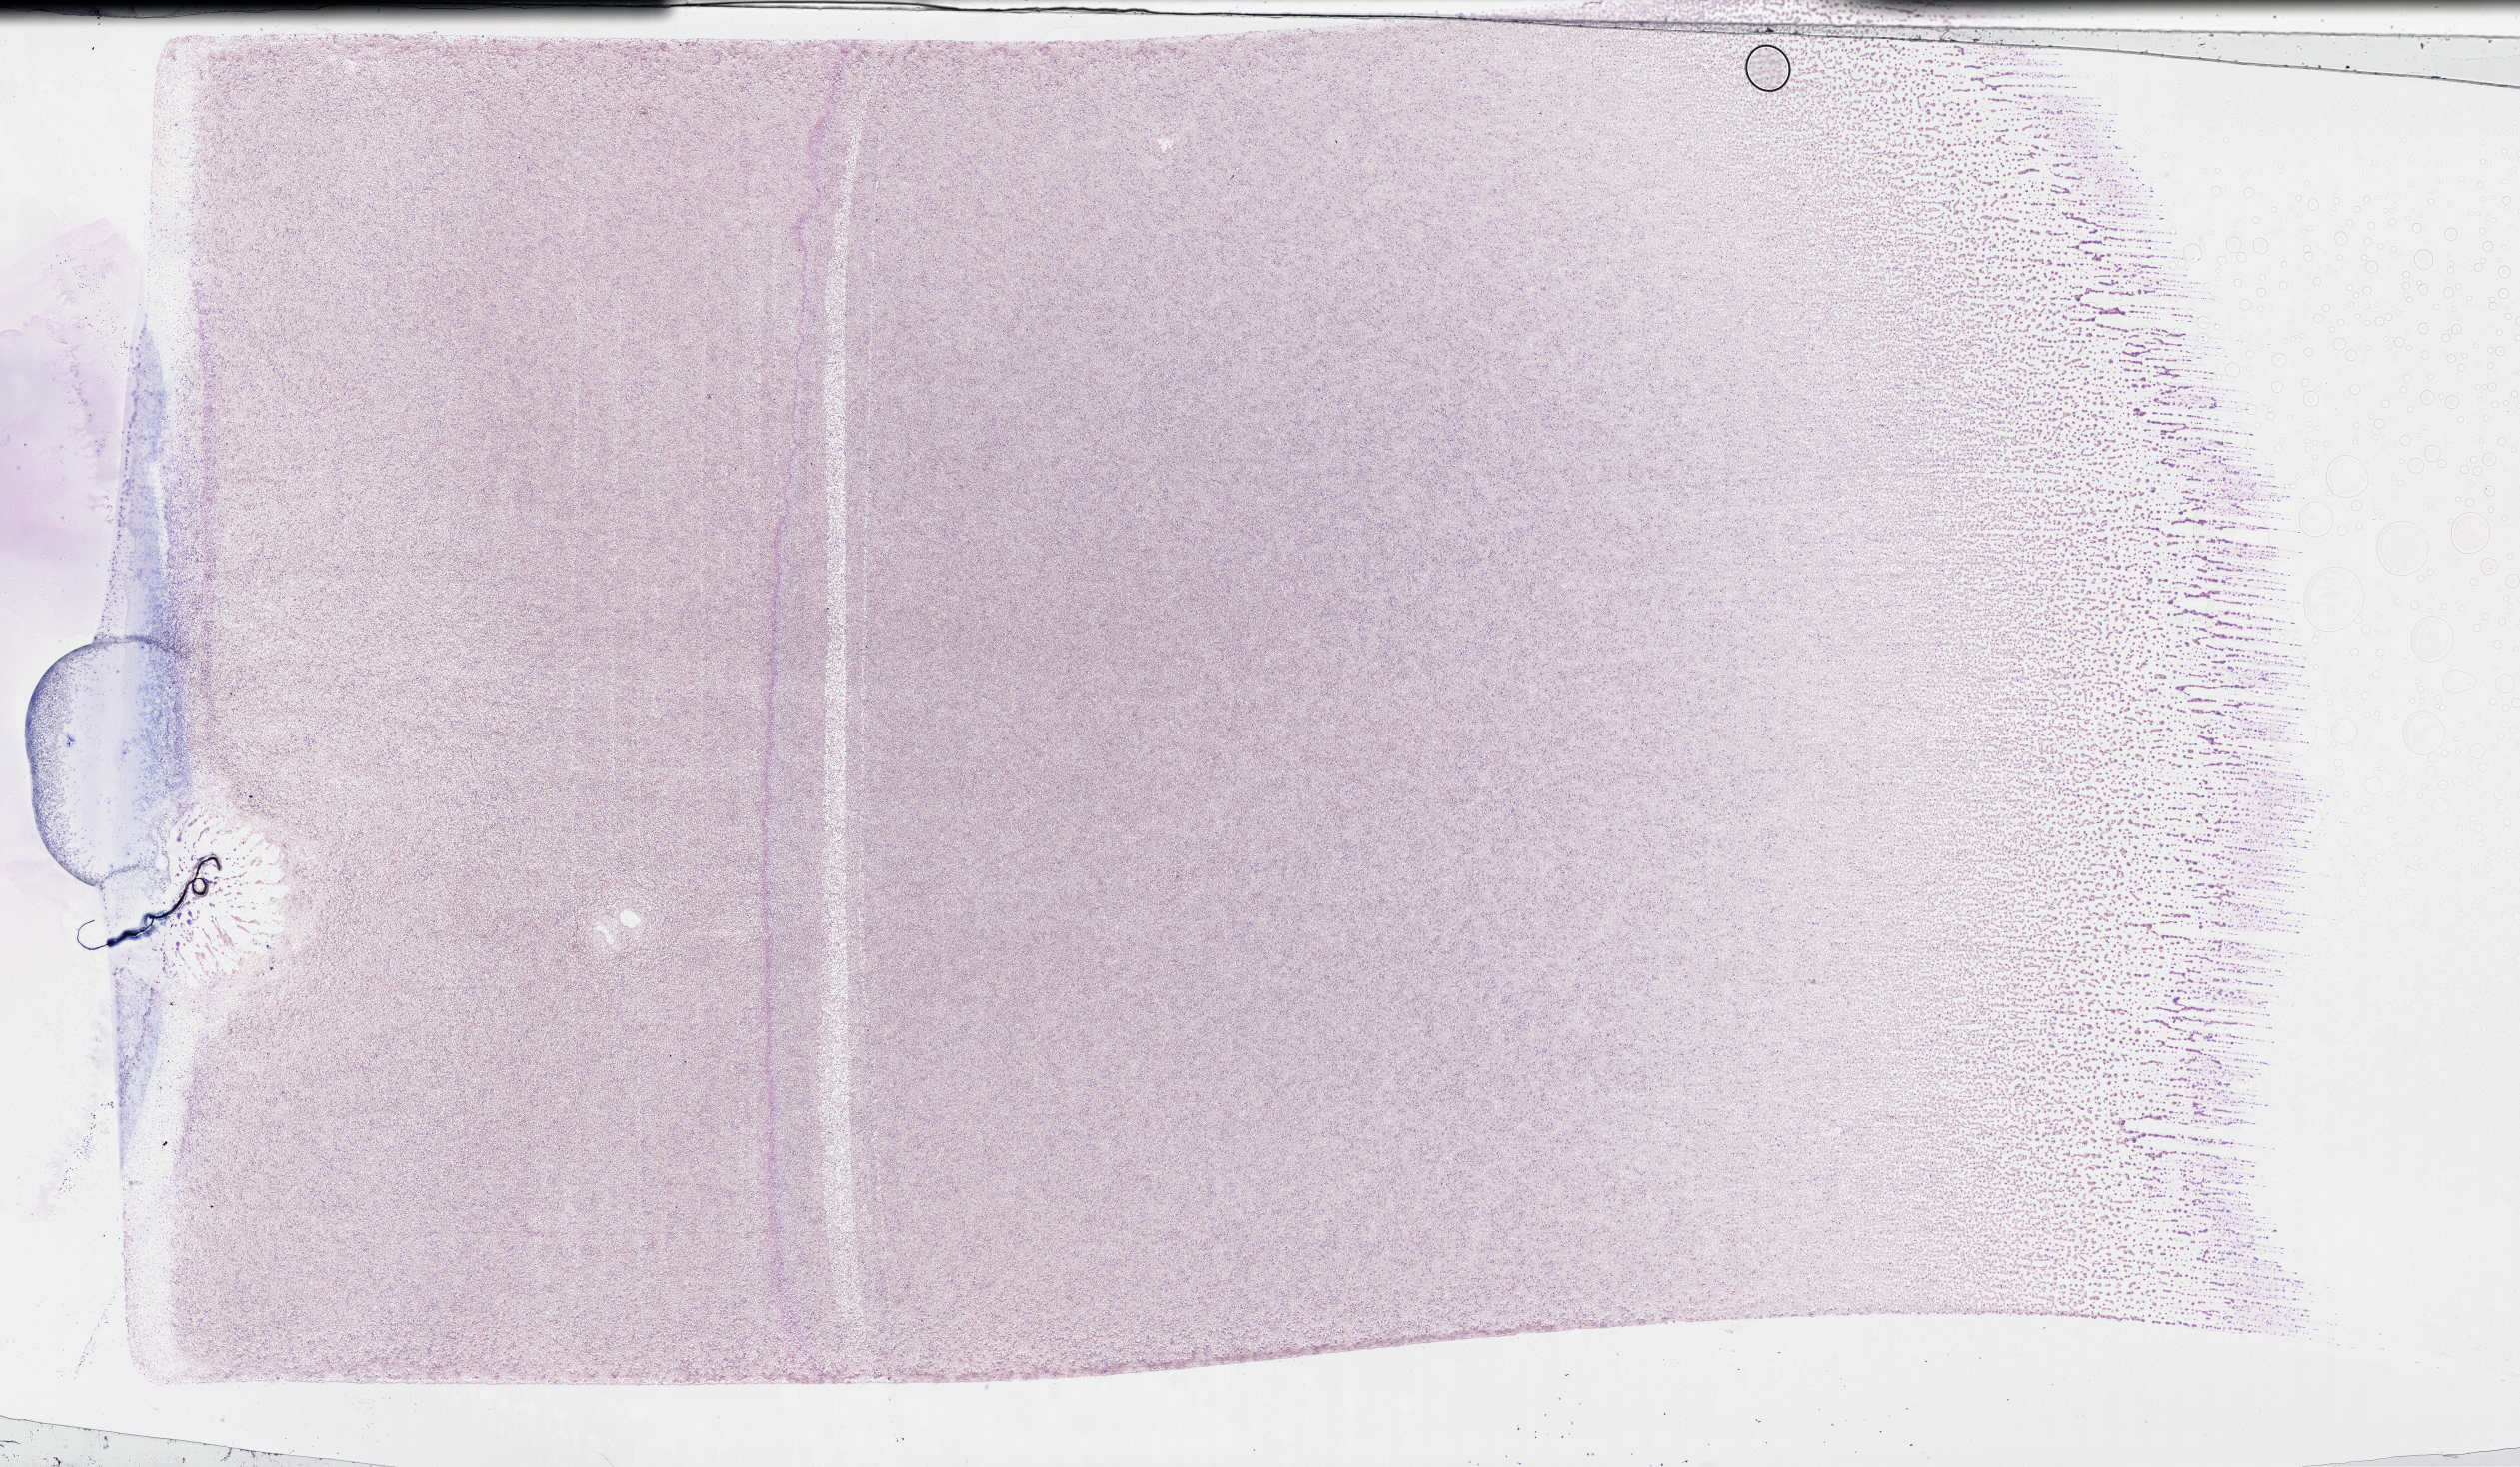
Digitized Hematoxylin and eosin (H&E) stained tissue section (whole slide) — a low-resolution overview of the entire scanned area, about 40.7 x 23.7 mm; peripheral blood (leukaemic) sample. Male, 63 y/o.
Diagnosis: Acute Myeloid Leukemia. WHO classification: AML with mutated NPM1. FAB classification: M1.